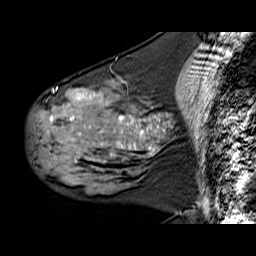
Breast MRI (dynamic contrast-enhanced), one sagittal slice. Slice 25 of 60 in the series (ordered by position). Dynamic contrast-enhanced series, time point 2 of 6 at this slice position (early post-contrast). 1.5 T. TE 6.3 ms, TR 32.9 ms. 4 mm slice thickness. 256 × 256 image matrix. Female patient. Case-level facts recorded for this patient, not image findings: setting: breast cancer imaged before/during neoadjuvant chemotherapy; receptor status: HER2-positive.
Annotated regions visible in this slice (semi-automatically segmented with operator editing):
- analysis volume of interest (the breast-tissue region the enhancement analysis was run in; not a lesion): box from (x=31, y=79) to (x=169, y=180) px
- tumour enhancement mask (voxels above the 100 % enhancement threshold inside the analysis volume of interest): (x=50, y=93)–(x=160, y=148)